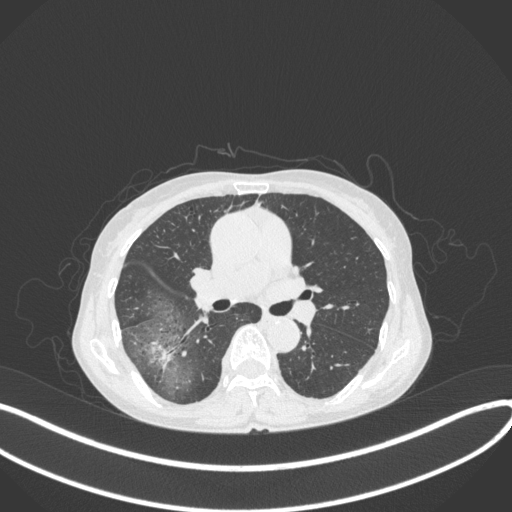
Chest CT, one axial slice; slice 229 of 379 in the series (ordered by position); reconstruction kernel B31f; lung window (W 1500 / L -600 HU); 512 × 512 image matrix, field of view 400 × 400 mm. Patient: female, 69 years. From the clinical record (not read from this slice): clinical TNM (as recorded): T1b N0 M0; histopathological grade: G2-3.
Outlined on this slice (bounding box drawn by a radiologist):
- lung tumour (recorded histology: adenocarcinoma): bounding box (x1, y1, x2, y2) in pixels: (142, 336, 176, 372)